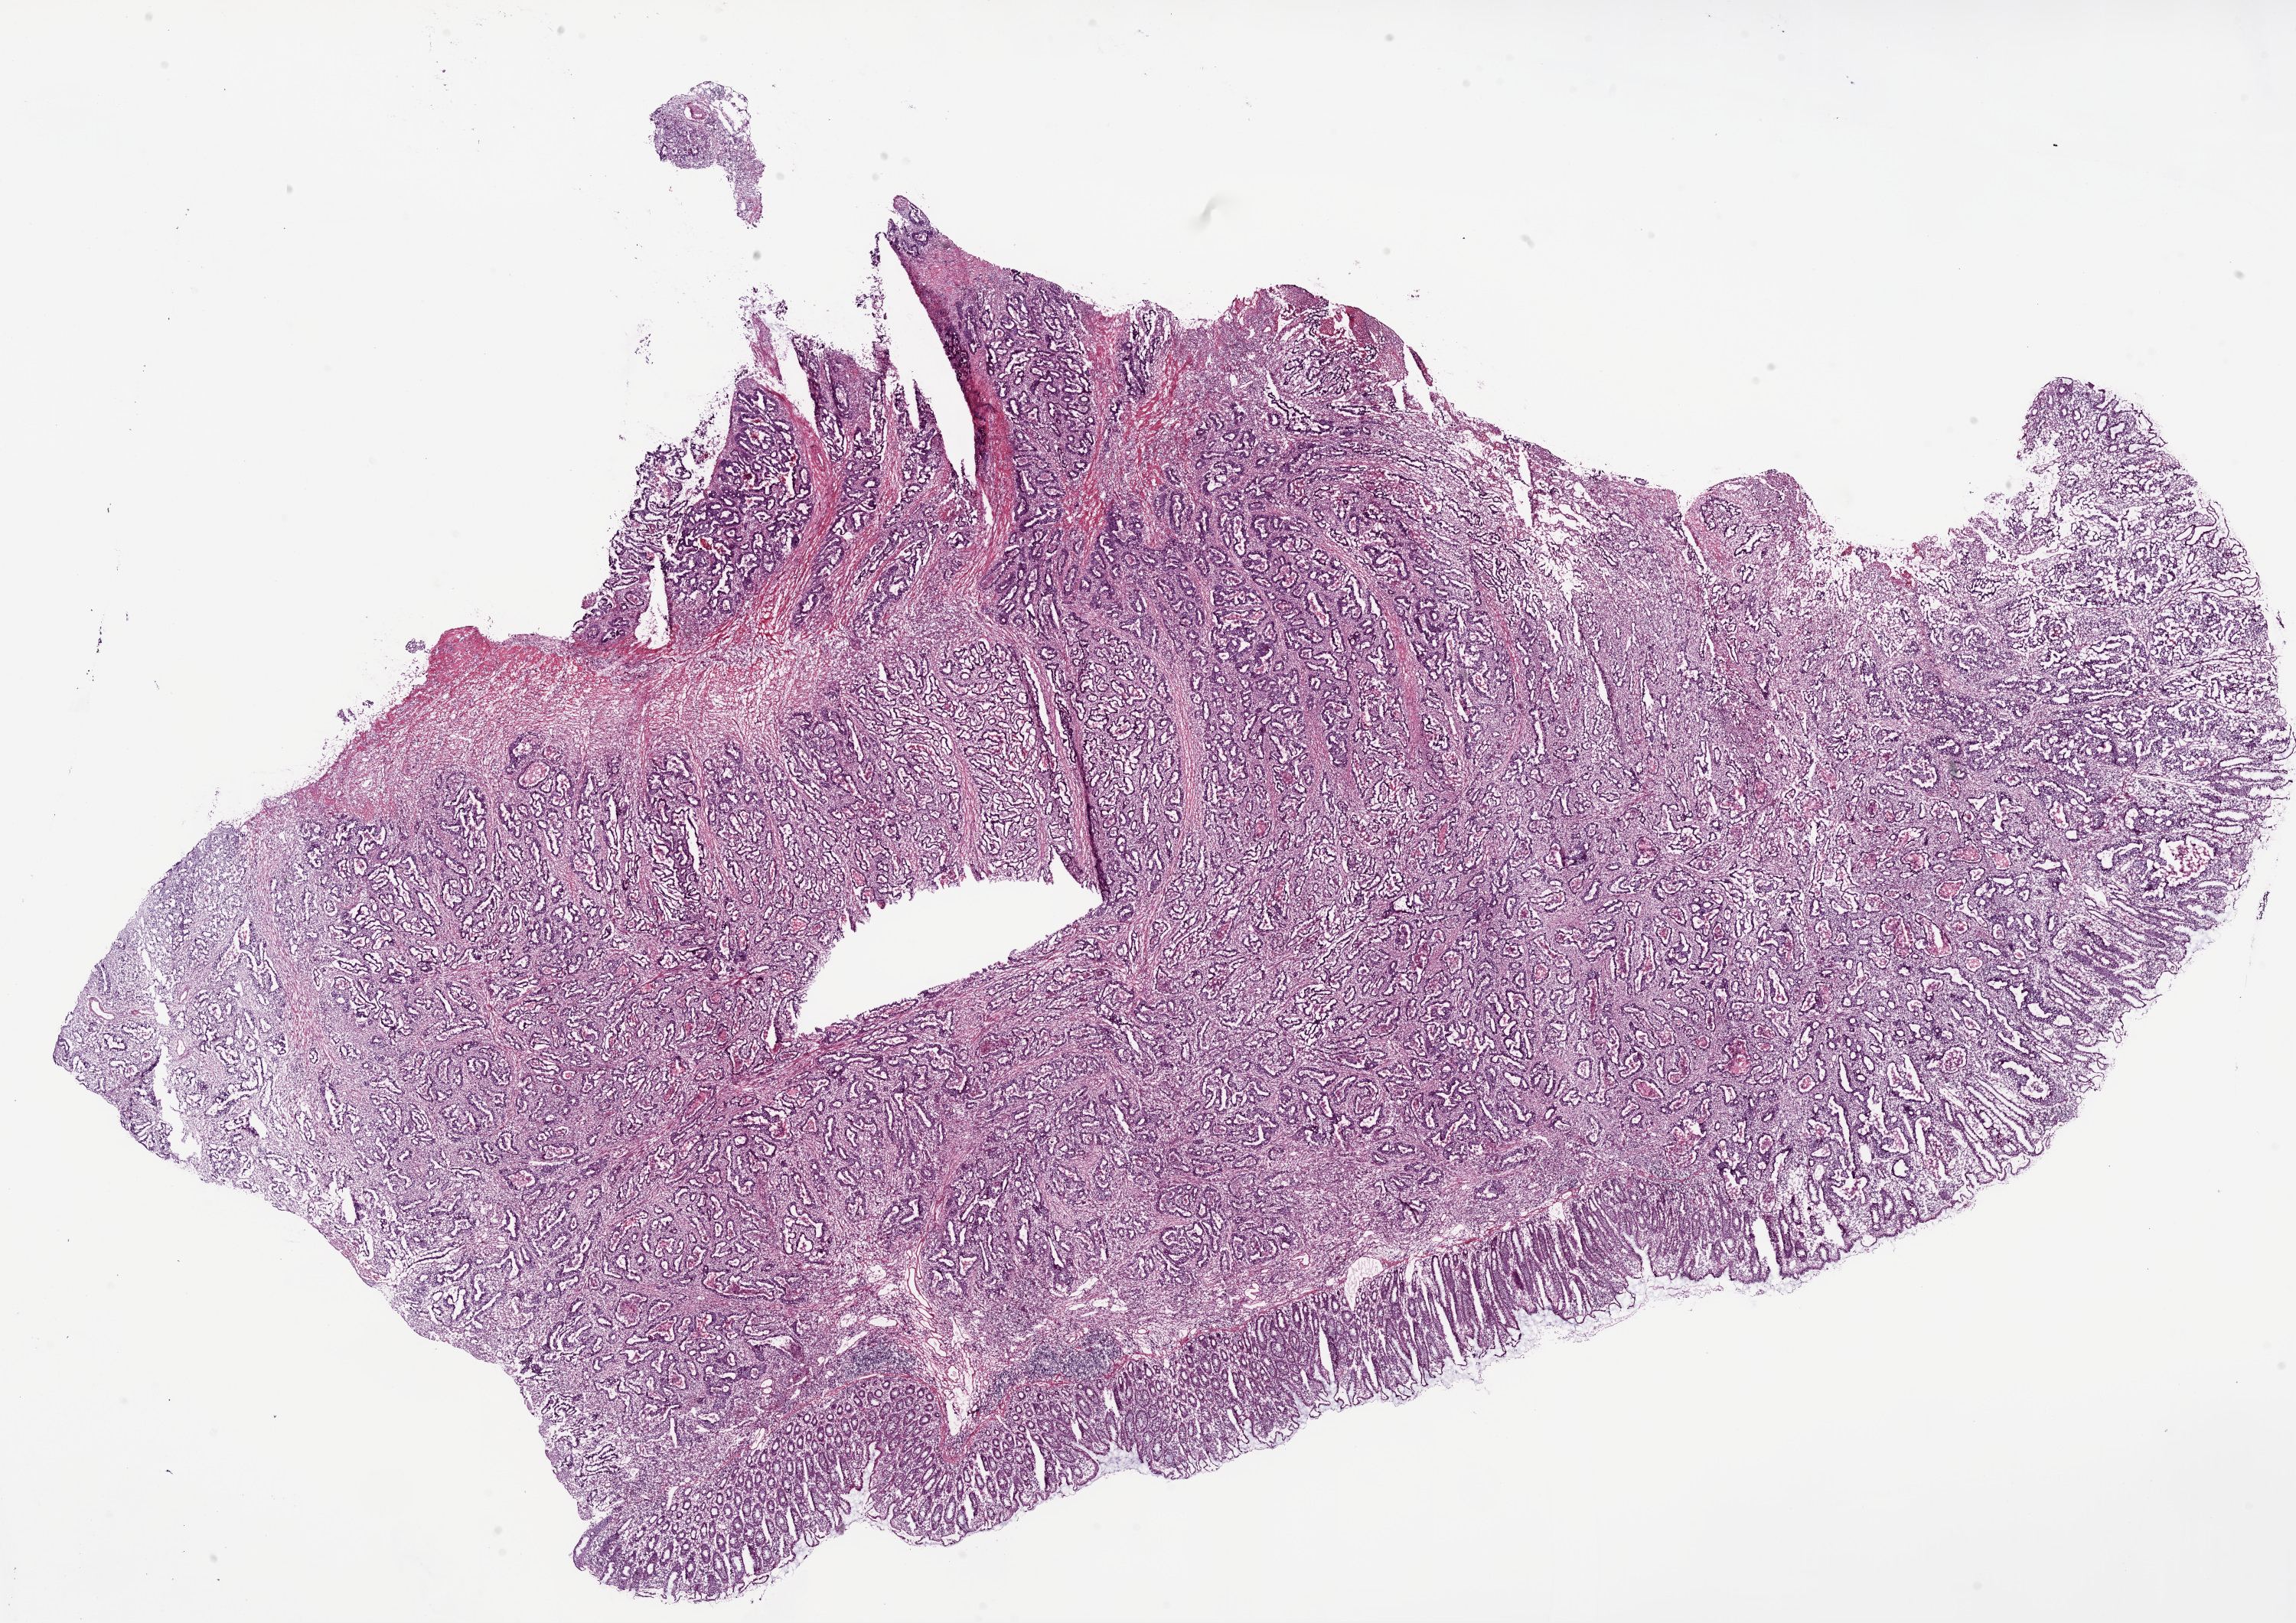
Hematoxylin and eosin (H&E) stained whole-slide image, a low-resolution overview of the entire scanned area, about 24.1 x 17.0 mm (from a 20x scan), frozen section from the bottom of the tissue portion, primary tumour sample from the colon. Male patient; age at initial diagnosis 58 years. Pathologist review of this section (percent, as recorded): tumour cells 65%, tumour nuclei 75%.
Pathologic diagnosis: Adenocarcinoma, NOS (ascending colon).